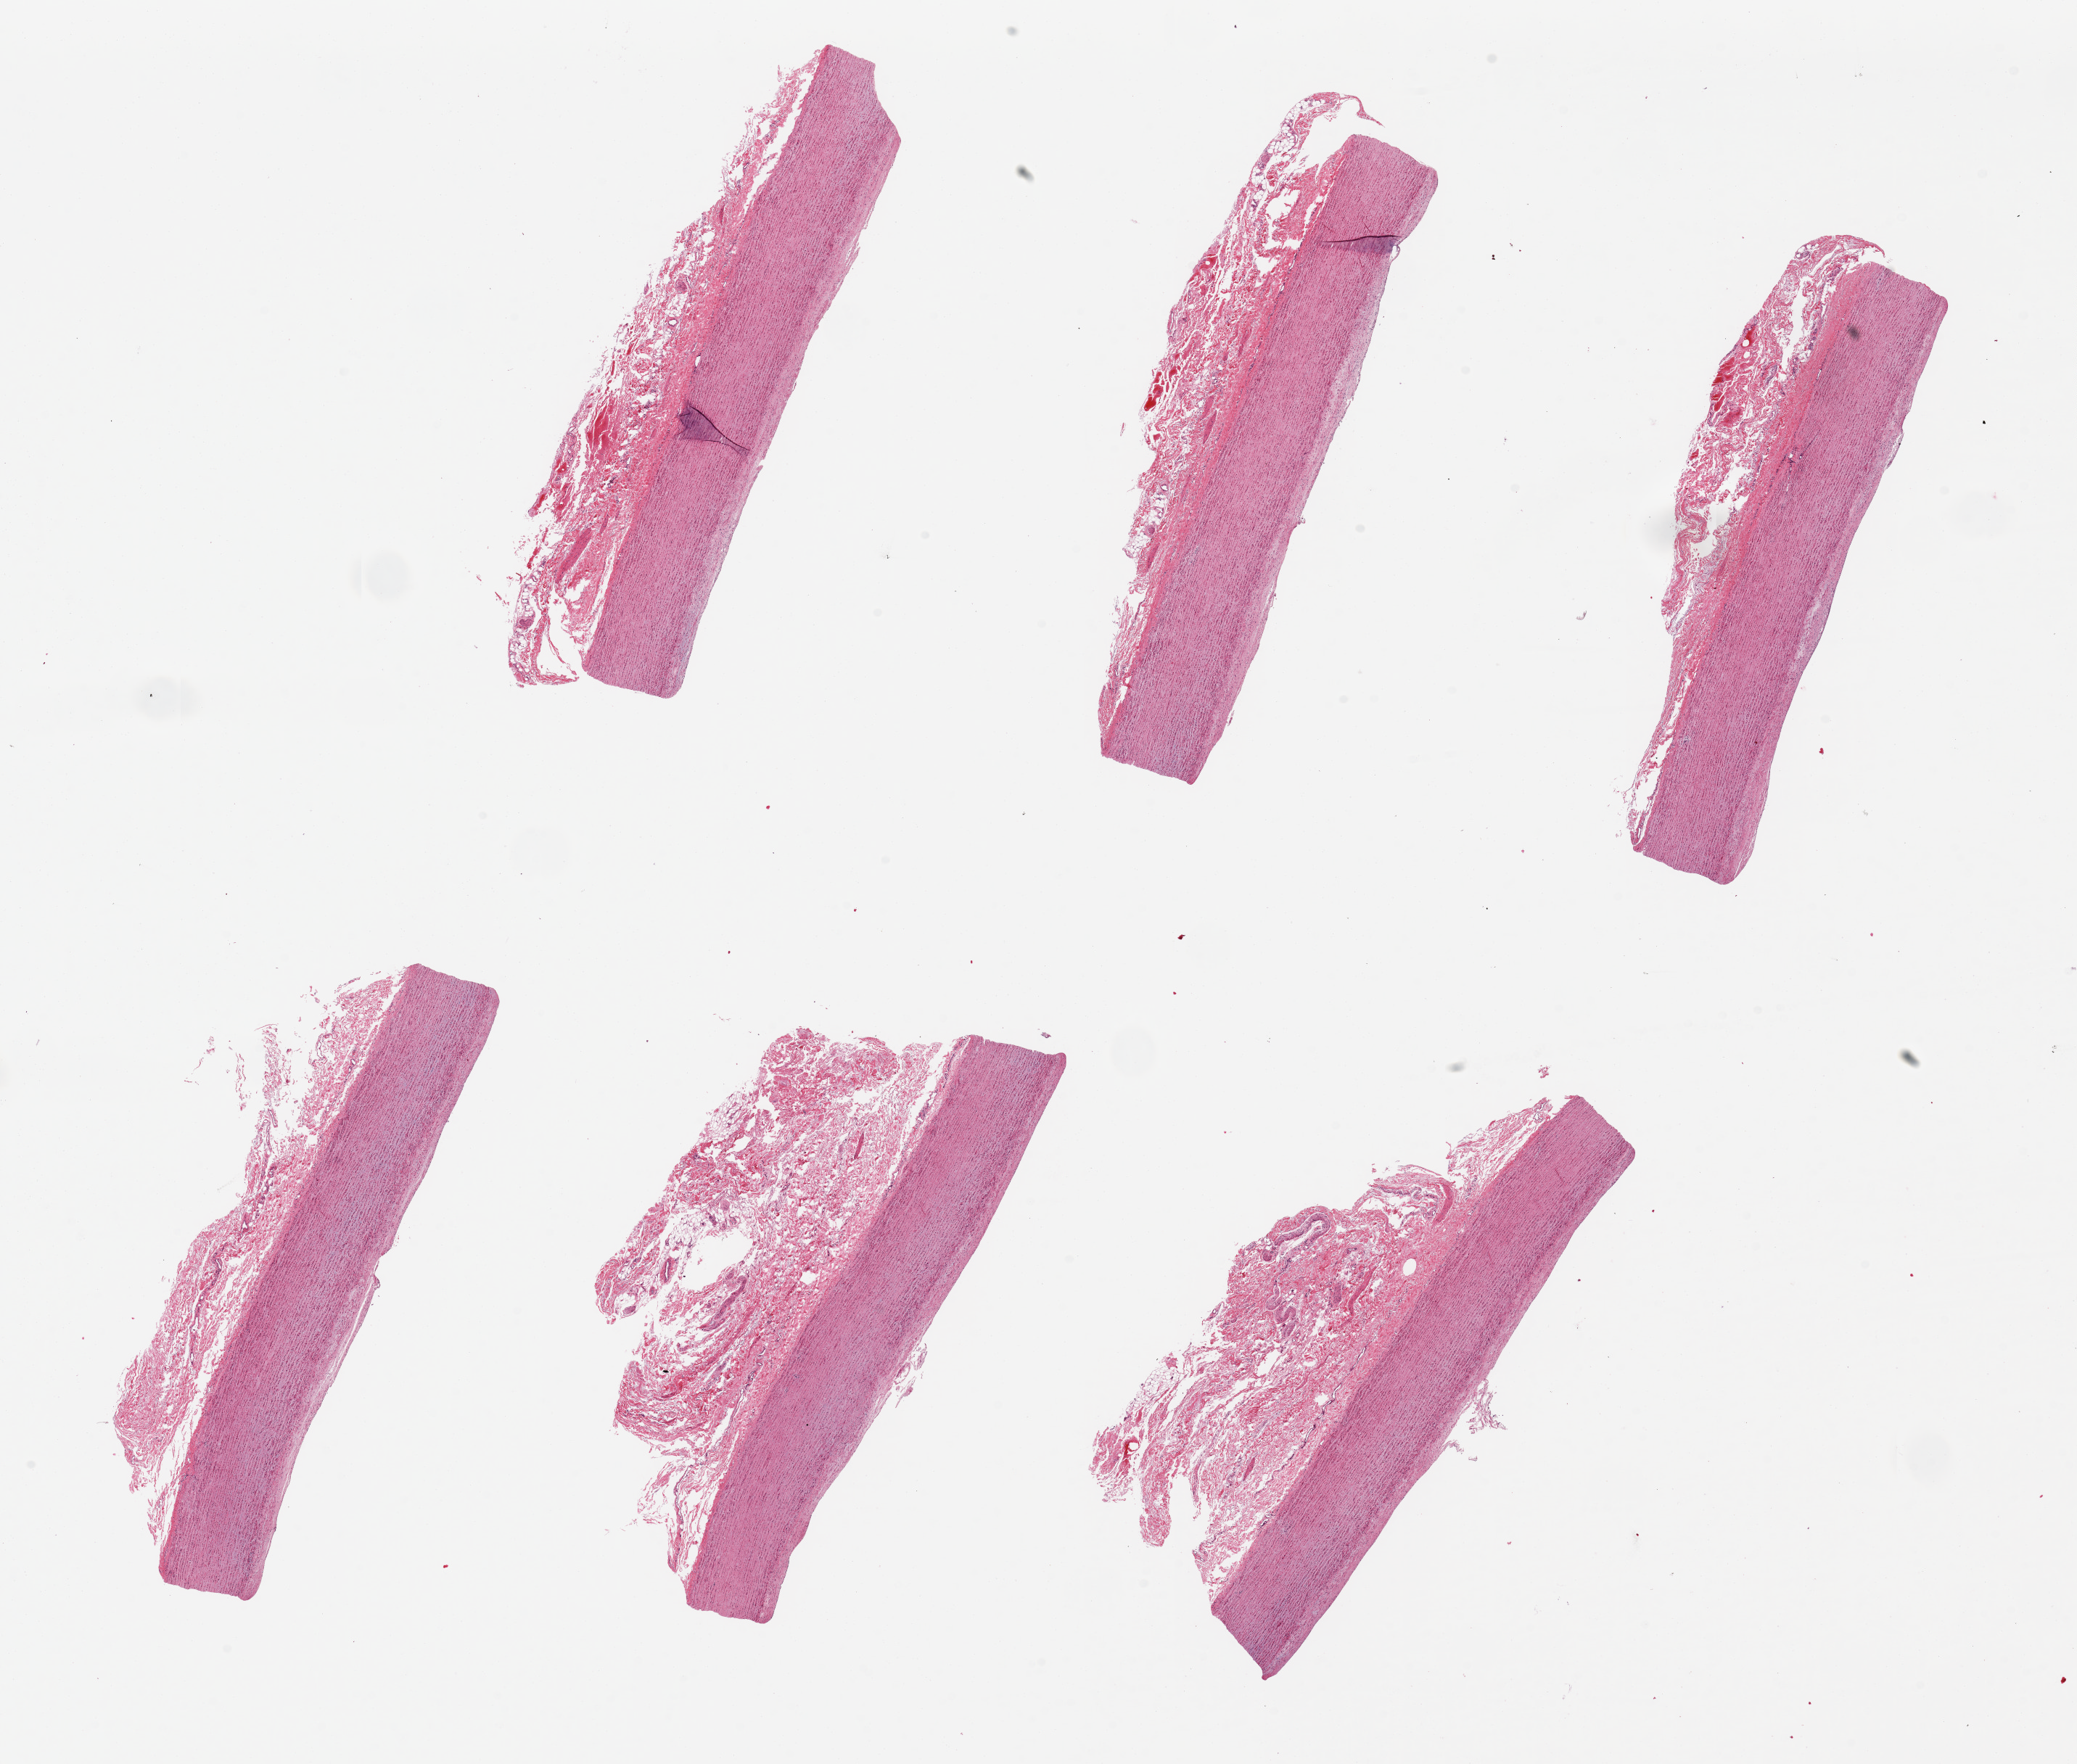
H&E whole-slide image — whole scanned area (about 22.6 x 19.2 mm) shown as a low-resolution overview. PAXgene-fixed paraffin-embedded (PFPE) section. Section of aorta (target tissue). Donor tissue sample. Donor sex: female.
* review note (as recorded): 6 pieces up to 7x1 mm; adventitial fibrous tissue up to 2 mm thick